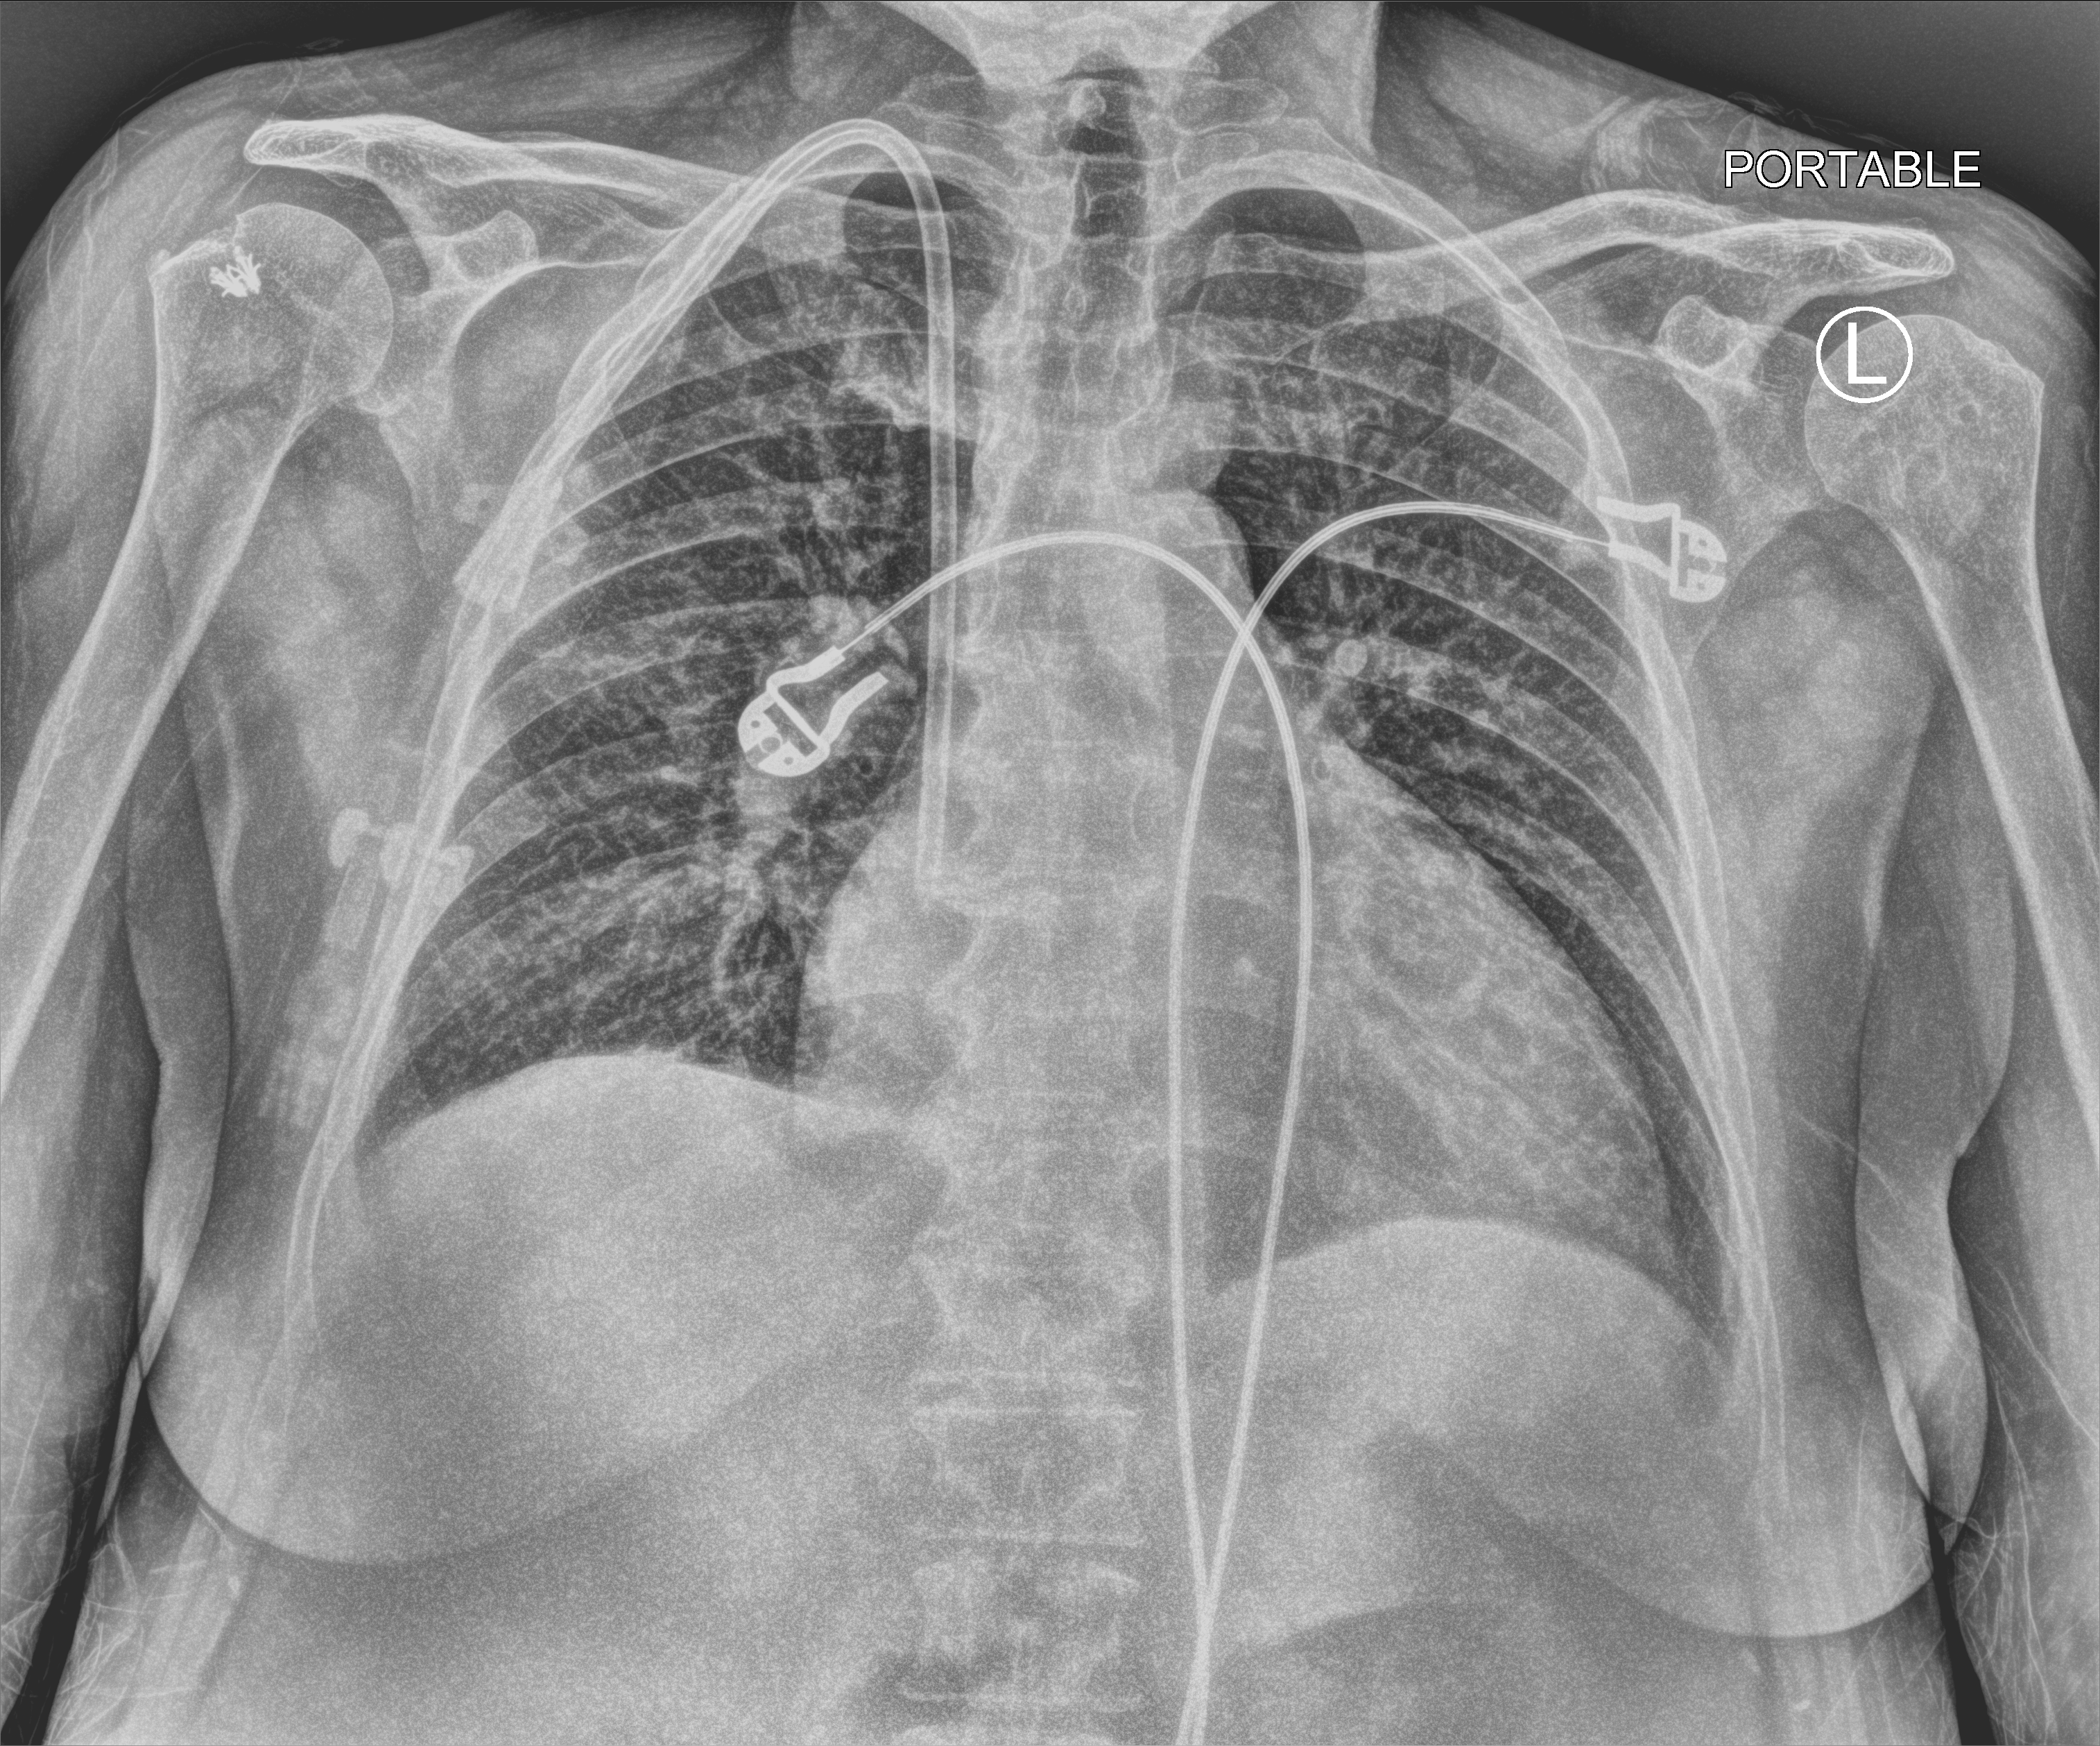
Chest X-ray (portable). Patient hospitalised with COVID-19; female, aged 60–74 years.
From the hospital-stay record, not from the radiograph (when in the stay this image was taken is not recorded): admitted to intensive care during this hospital stay: no; mechanically ventilated during this hospital stay: no; length of hospital stay: 2 days.